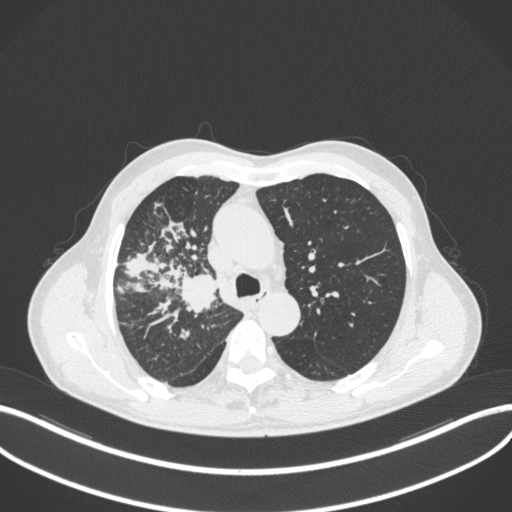
Chest CT, one axial slice; reconstruction kernel B31f; 120 kVp; lung window (W 1500 / L -600 HU); 512 × 512 image matrix. Male patient, age 69 years. From the clinical record (not read from this slice): clinical TNM (as recorded): T2a N0 M0.
Annotated regions visible in this slice (bounding box drawn by a radiologist):
- lung tumour (recorded histology: adenocarcinoma): bounding box (x1, y1, x2, y2) in pixels: (177, 272, 219, 315)